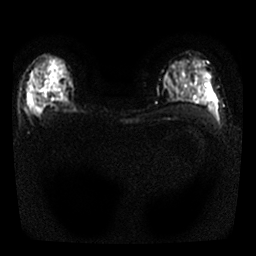
Breast MRI, one axial slice. Slice 17 of 25 in the series (ordered by position). Diffusion-weighted series; image 2 of 4 stored at this slice position (different b-values; order by instance number). 1.5 T. 256 × 256 image matrix. Female patient.
Structures marked on this image (outlined manually by an expert reader):
- tumour on diffusion-weighted imaging: box from (x=27, y=93) to (x=38, y=112) px